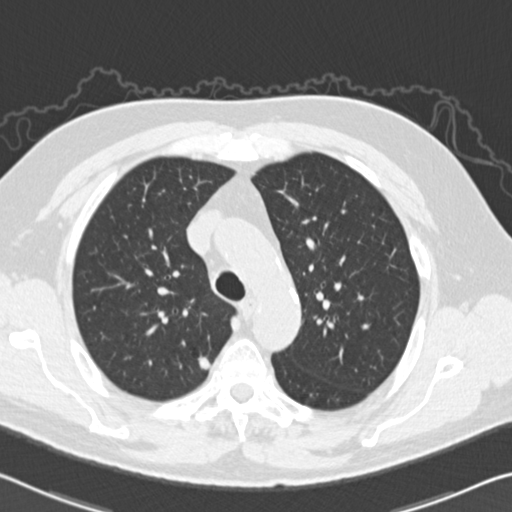
Chest CT (low-dose screening protocol), one axial image, baseline annual screen, lung window (W 1500 / L -600 HU), 2 mm slice thickness, slice 39 of 151 in the series, 512 × 512 image matrix, field of view 340 × 340 mm. Male, age 64 years at enrolment. Former smoker at enrolment.
• Expert reader's lesion annotation, bounding box (x1, y1, x2, y2) in pixels: (185, 341, 229, 386).
• The exam's reader record, not a measurement of the box and not confirmed to be the same lesion: non-calcified nodule or mass ≥4 mm, right upper lobe, 10 × 8 mm, spiculated (stellate) margins, soft tissue attenuation.
• Official screen result: positive, change unspecified: nodule(s) >= 4 mm or enlarging nodule(s), mass(es), or other non-specific abnormalities suspicious for lung cancer.
• Lung cancer was diagnosed 99 days after this screen: adenocarcinoma, NOS, right upper lobe, poorly differentiated (G3), stage IA (AJCC 6th edition), 11 mm at pathology.